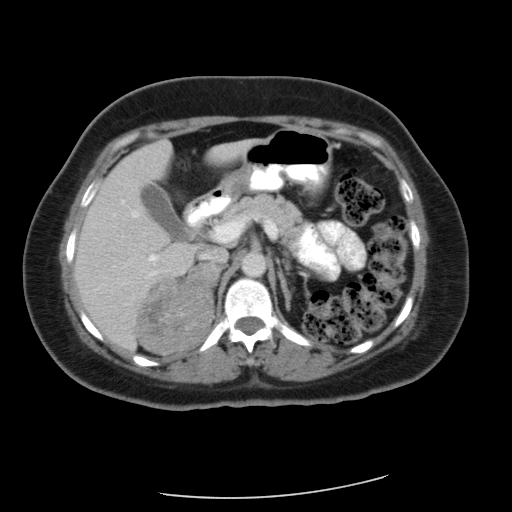
Contrast-enhanced abdominal CT, one axial slice; position 37 of 56 along the scan axis; reconstruction kernel FC12; 120 kVp; soft-tissue window (W 400 / L 40 HU); 5 mm slice thickness; 512 × 512 image matrix, field of view 400 × 400 mm. Female patient, age 58 years. From the clinical record (not read from this slice): diagnosis: adrenocortical carcinoma; tumour side: right adrenal; tumour size at pathology: 9 cm; Ki-67 index: 25 %; stage (as recorded): 3.
Structures marked on this image (semi-automatically segmented with operator editing):
- mass: bounding box <139,266,218,353> (left, top, right, bottom; pixels)